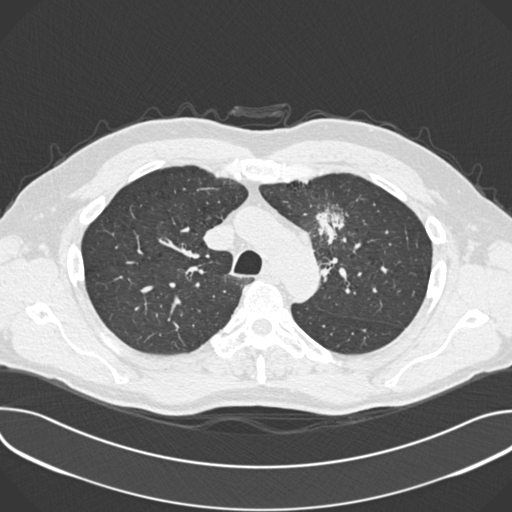
Low-dose screening chest CT, one axial slice; slice 270 of 361 in the series (ordered by position); 120 kVp; lung window (W 1500 / L -600 HU); 1 mm slice thickness; 512 × 512 image matrix, field of view 380 × 380 mm.
Outlined on this slice (manually delineated by an expert):
- lesion 1 (tumor, upper lobe of left lung): box from (x=316, y=209) to (x=344, y=239) px